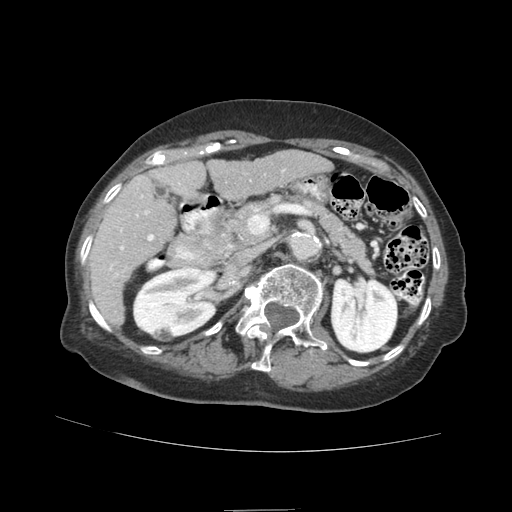
Contrast-enhanced abdominal CT (liver protocol), one axial slice. Position 42 of 89 along the scan axis. Reconstruction kernel STANDARD. 140 kVp. Soft-tissue window (W 400 / L 40 HU). 2.5 mm slice thickness. 512 × 512 image matrix. Case-level facts recorded for this patient, not image findings: diagnosis: hepatocellular carcinoma (patient treated with transarterial chemoembolisation; whether this scan precedes or follows treatment is not stated here); TNM stage (as recorded): Stage-II; Child-Pugh class: A; tumour nodularity: multinodular; tumour size: 4 cm.
Outlined on this slice (semi-automatic segmentation, software-assisted and operator-edited):
- liver parenchyma outside the tumour (the mass and vessels are separate outlines, so this box may not span the whole liver): bounding box <90,150,332,324> (left, top, right, bottom; pixels)
- liver vessels: <109,169,285,277>